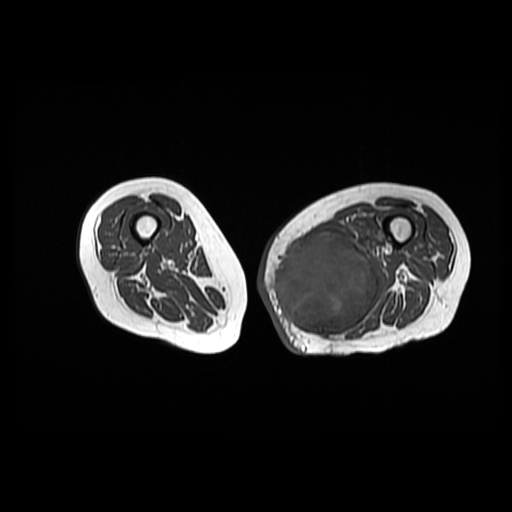
MRI of an extremity soft-tissue mass, one axial slice. Slice 31 of 42 in the series (ordered by position). 6 mm slice thickness. 512 × 512 image matrix. Female patient. Case-level facts recorded for this patient, not image findings: histological type: pleomorphic leiomyosarcoma; grade: high; site of the primary tumour: left thigh.
Structures marked on this image (outlined manually by an expert reader):
- gross tumour volume including surrounding oedema: bounding box (x1, y1, x2, y2) in pixels: (263, 230, 384, 338)
- gross tumour volume (mass): (263, 231, 378, 338)